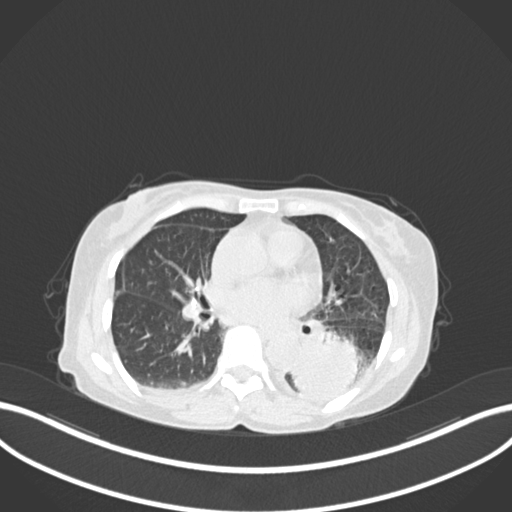
Chest CT, one axial slice; position 74 of 233 along the scan axis; reconstruction kernel B30f; lung window (W 1500 / L -600 HU); 1 mm slice thickness; 512 × 512 image matrix. Patient: female, 78 years. Case-level facts recorded for this patient, not image findings: clinical TNM (as recorded): T3 N0 M1.
Structures marked on this image (bounding box drawn by a radiologist):
- lung tumour (recorded histology: squamous cell carcinoma): box from (x=283, y=328) to (x=366, y=400) px